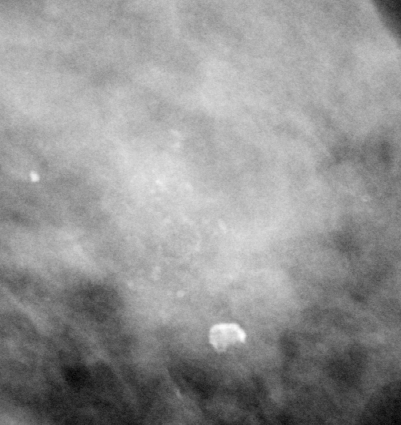
Region of interest cut from a scanned film mammogram (one marked finding), left breast, MLO view.
Finding: calcifications, morphology amorphous, distribution clustered; BI-RADS assessment category 5; pathology (as recorded): malignant.